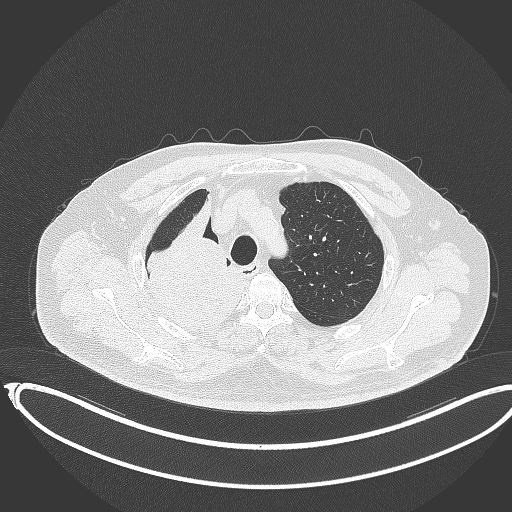
Chest CT, one axial slice; slice 293 of 403 in the series (ordered by position); reconstruction kernel B70f; 120 kVp; lung window (W 1500 / L -600 HU); 1 mm slice thickness; 512 × 512 image matrix, field of view 436 × 436 mm. Patient: male, 68 years. Case-level facts recorded for this patient, not image findings: clinical TNM (as recorded): T2a N0 M0.
Annotated regions visible in this slice (bounding box drawn by a radiologist):
- lung tumour (recorded histology: adenocarcinoma): bounding box <138,193,246,335> (left, top, right, bottom; pixels)